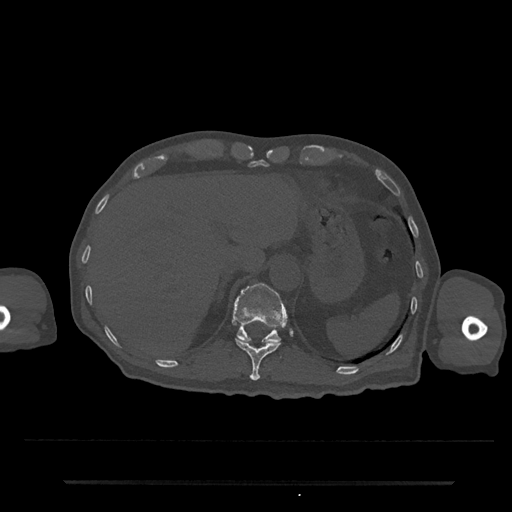
CT including the spine, one axial slice; position 230 of 797 along the scan axis; reconstruction kernel Br40s/3; 120 kVp; bone window (W 1800 / L 400 HU); 512 × 512 image matrix. Male patient, age 74 years. Case-level facts recorded for this patient, not image findings: primary cancer: prostate.
Outlined on this slice (semi-automatically segmented with operator editing):
- T11 vertebra: bounding box <235,338,281,381> (left, top, right, bottom; pixels)
- T12 vertebra: <233,283,286,343>